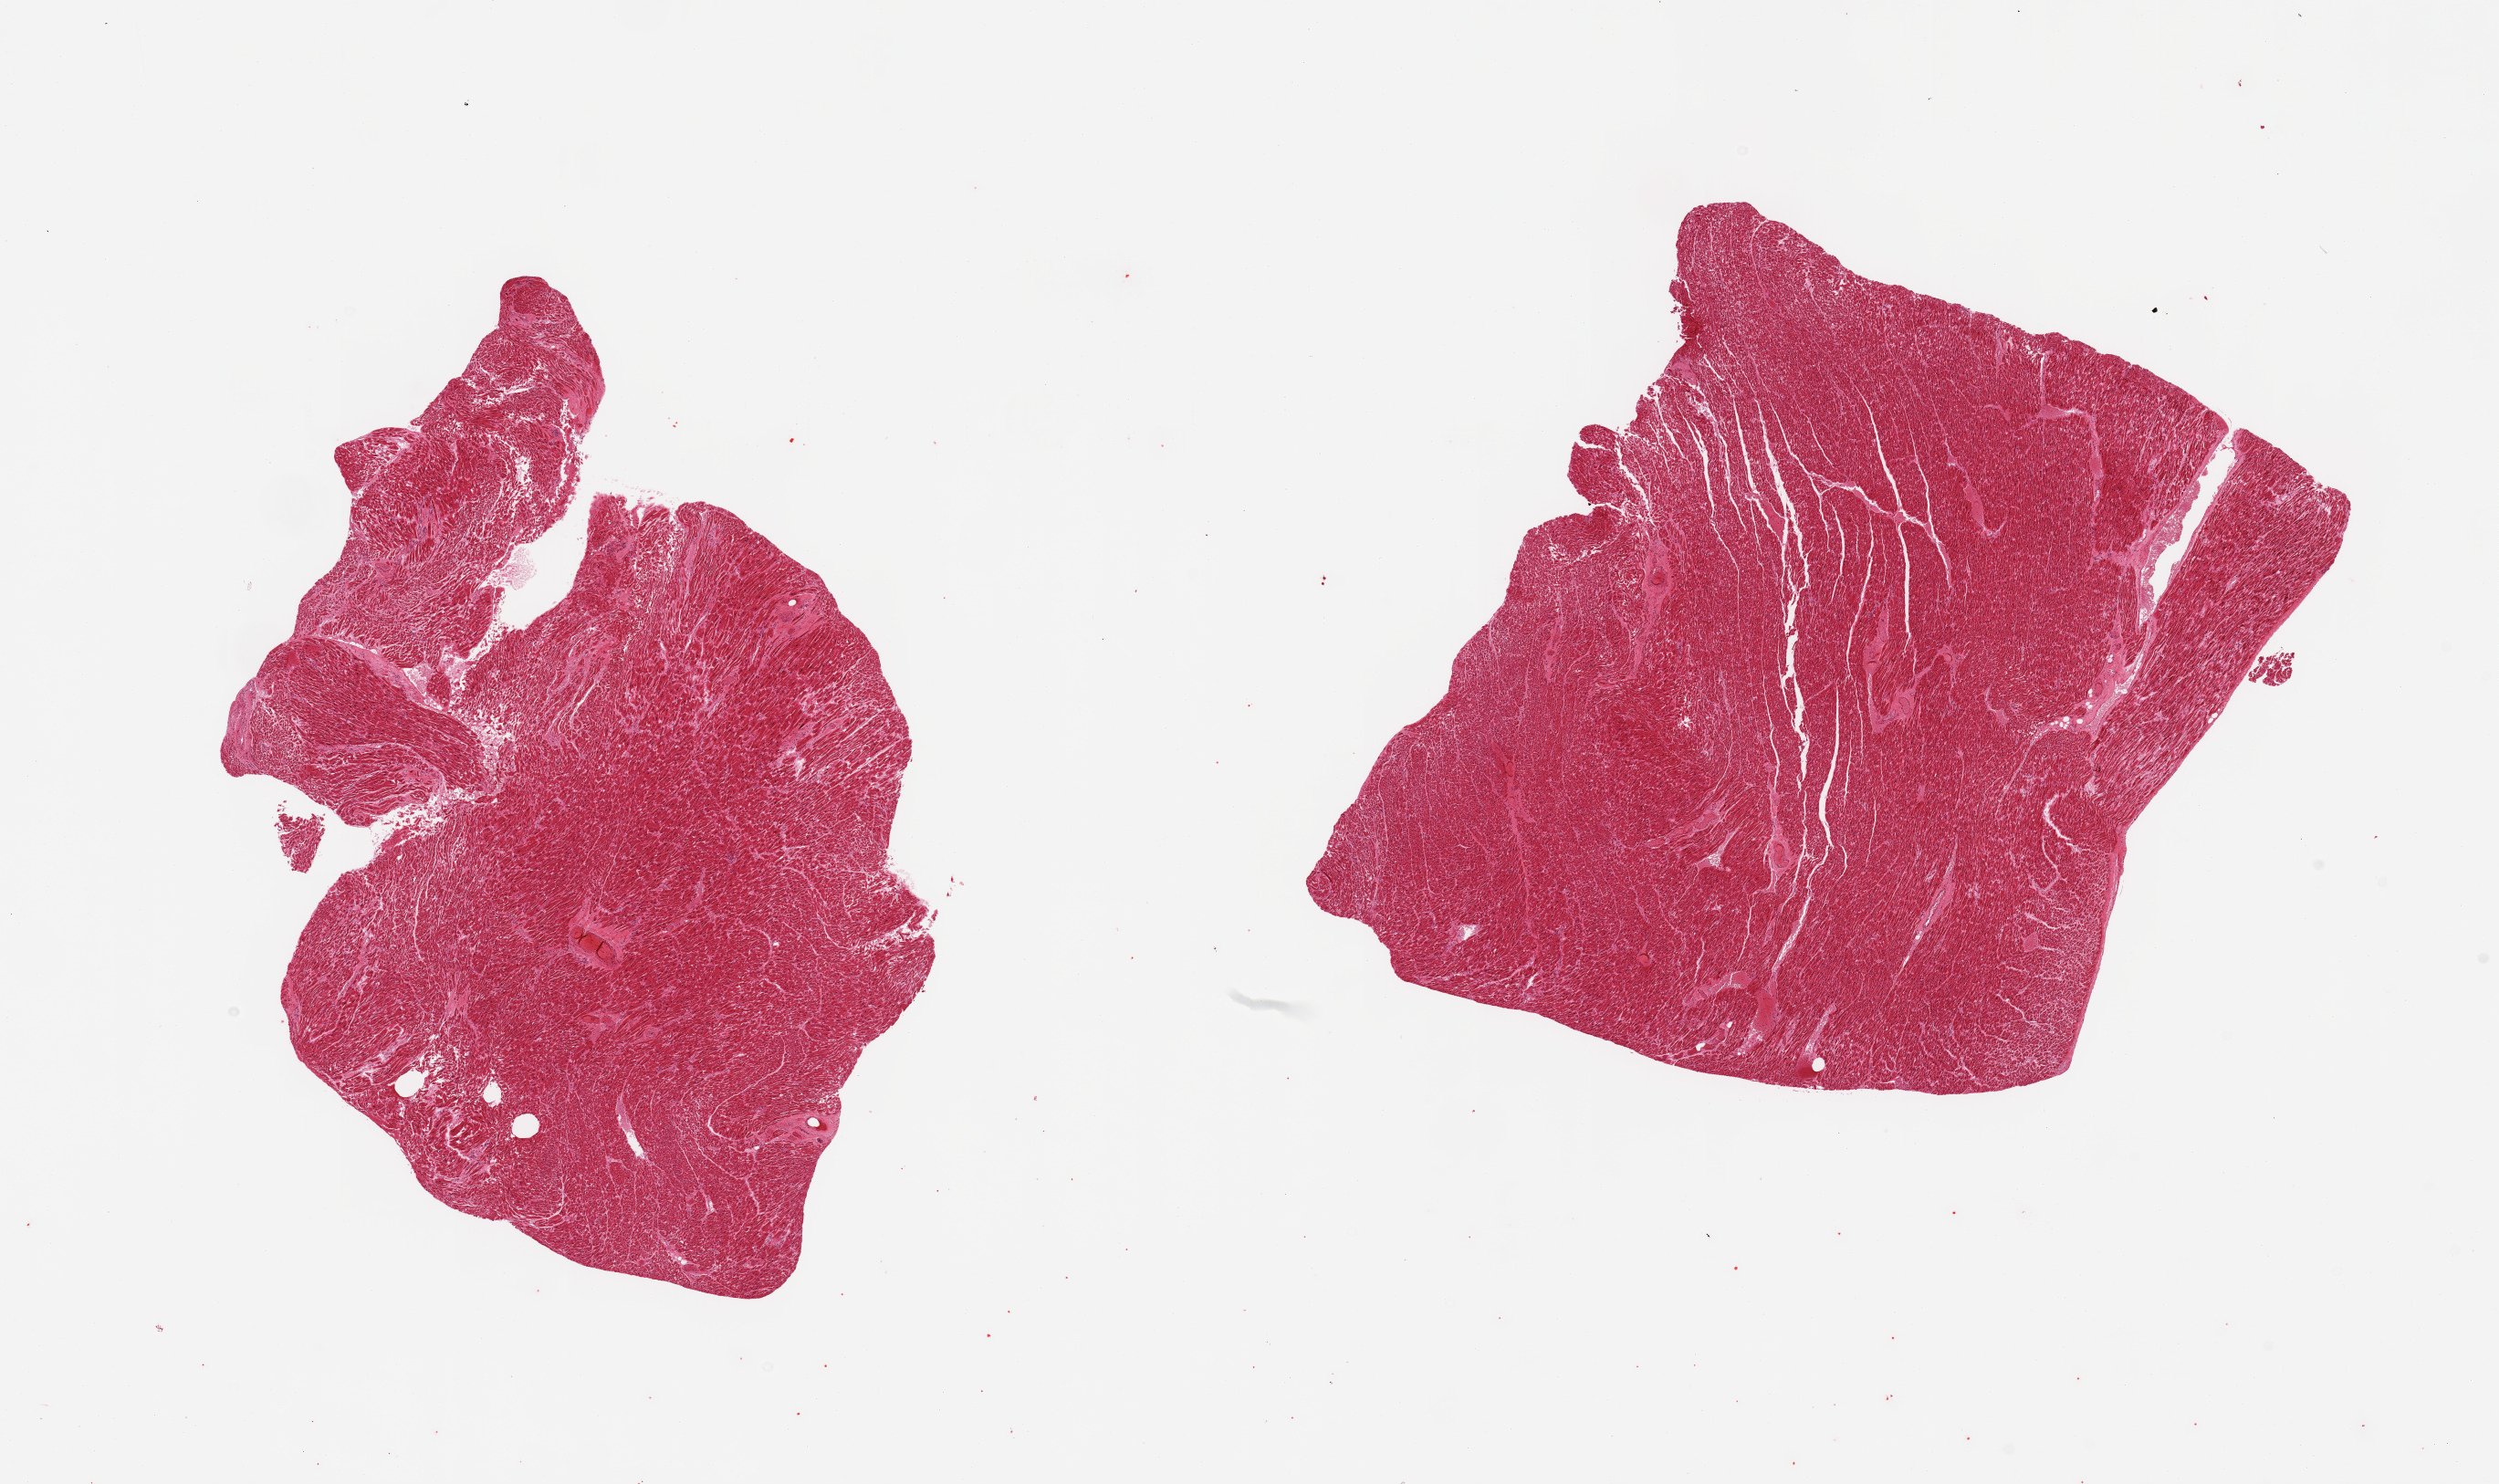
H&E whole-slide image, low-resolution overview of the scanned area, about 21.7 x 12.9 mm; PAXgene-fixed, paraffin-embedded tissue; target tissue: heart; tissue donor sample.
Pathologist's review note for this sample: 2 pieces; well dissected; no lesions.